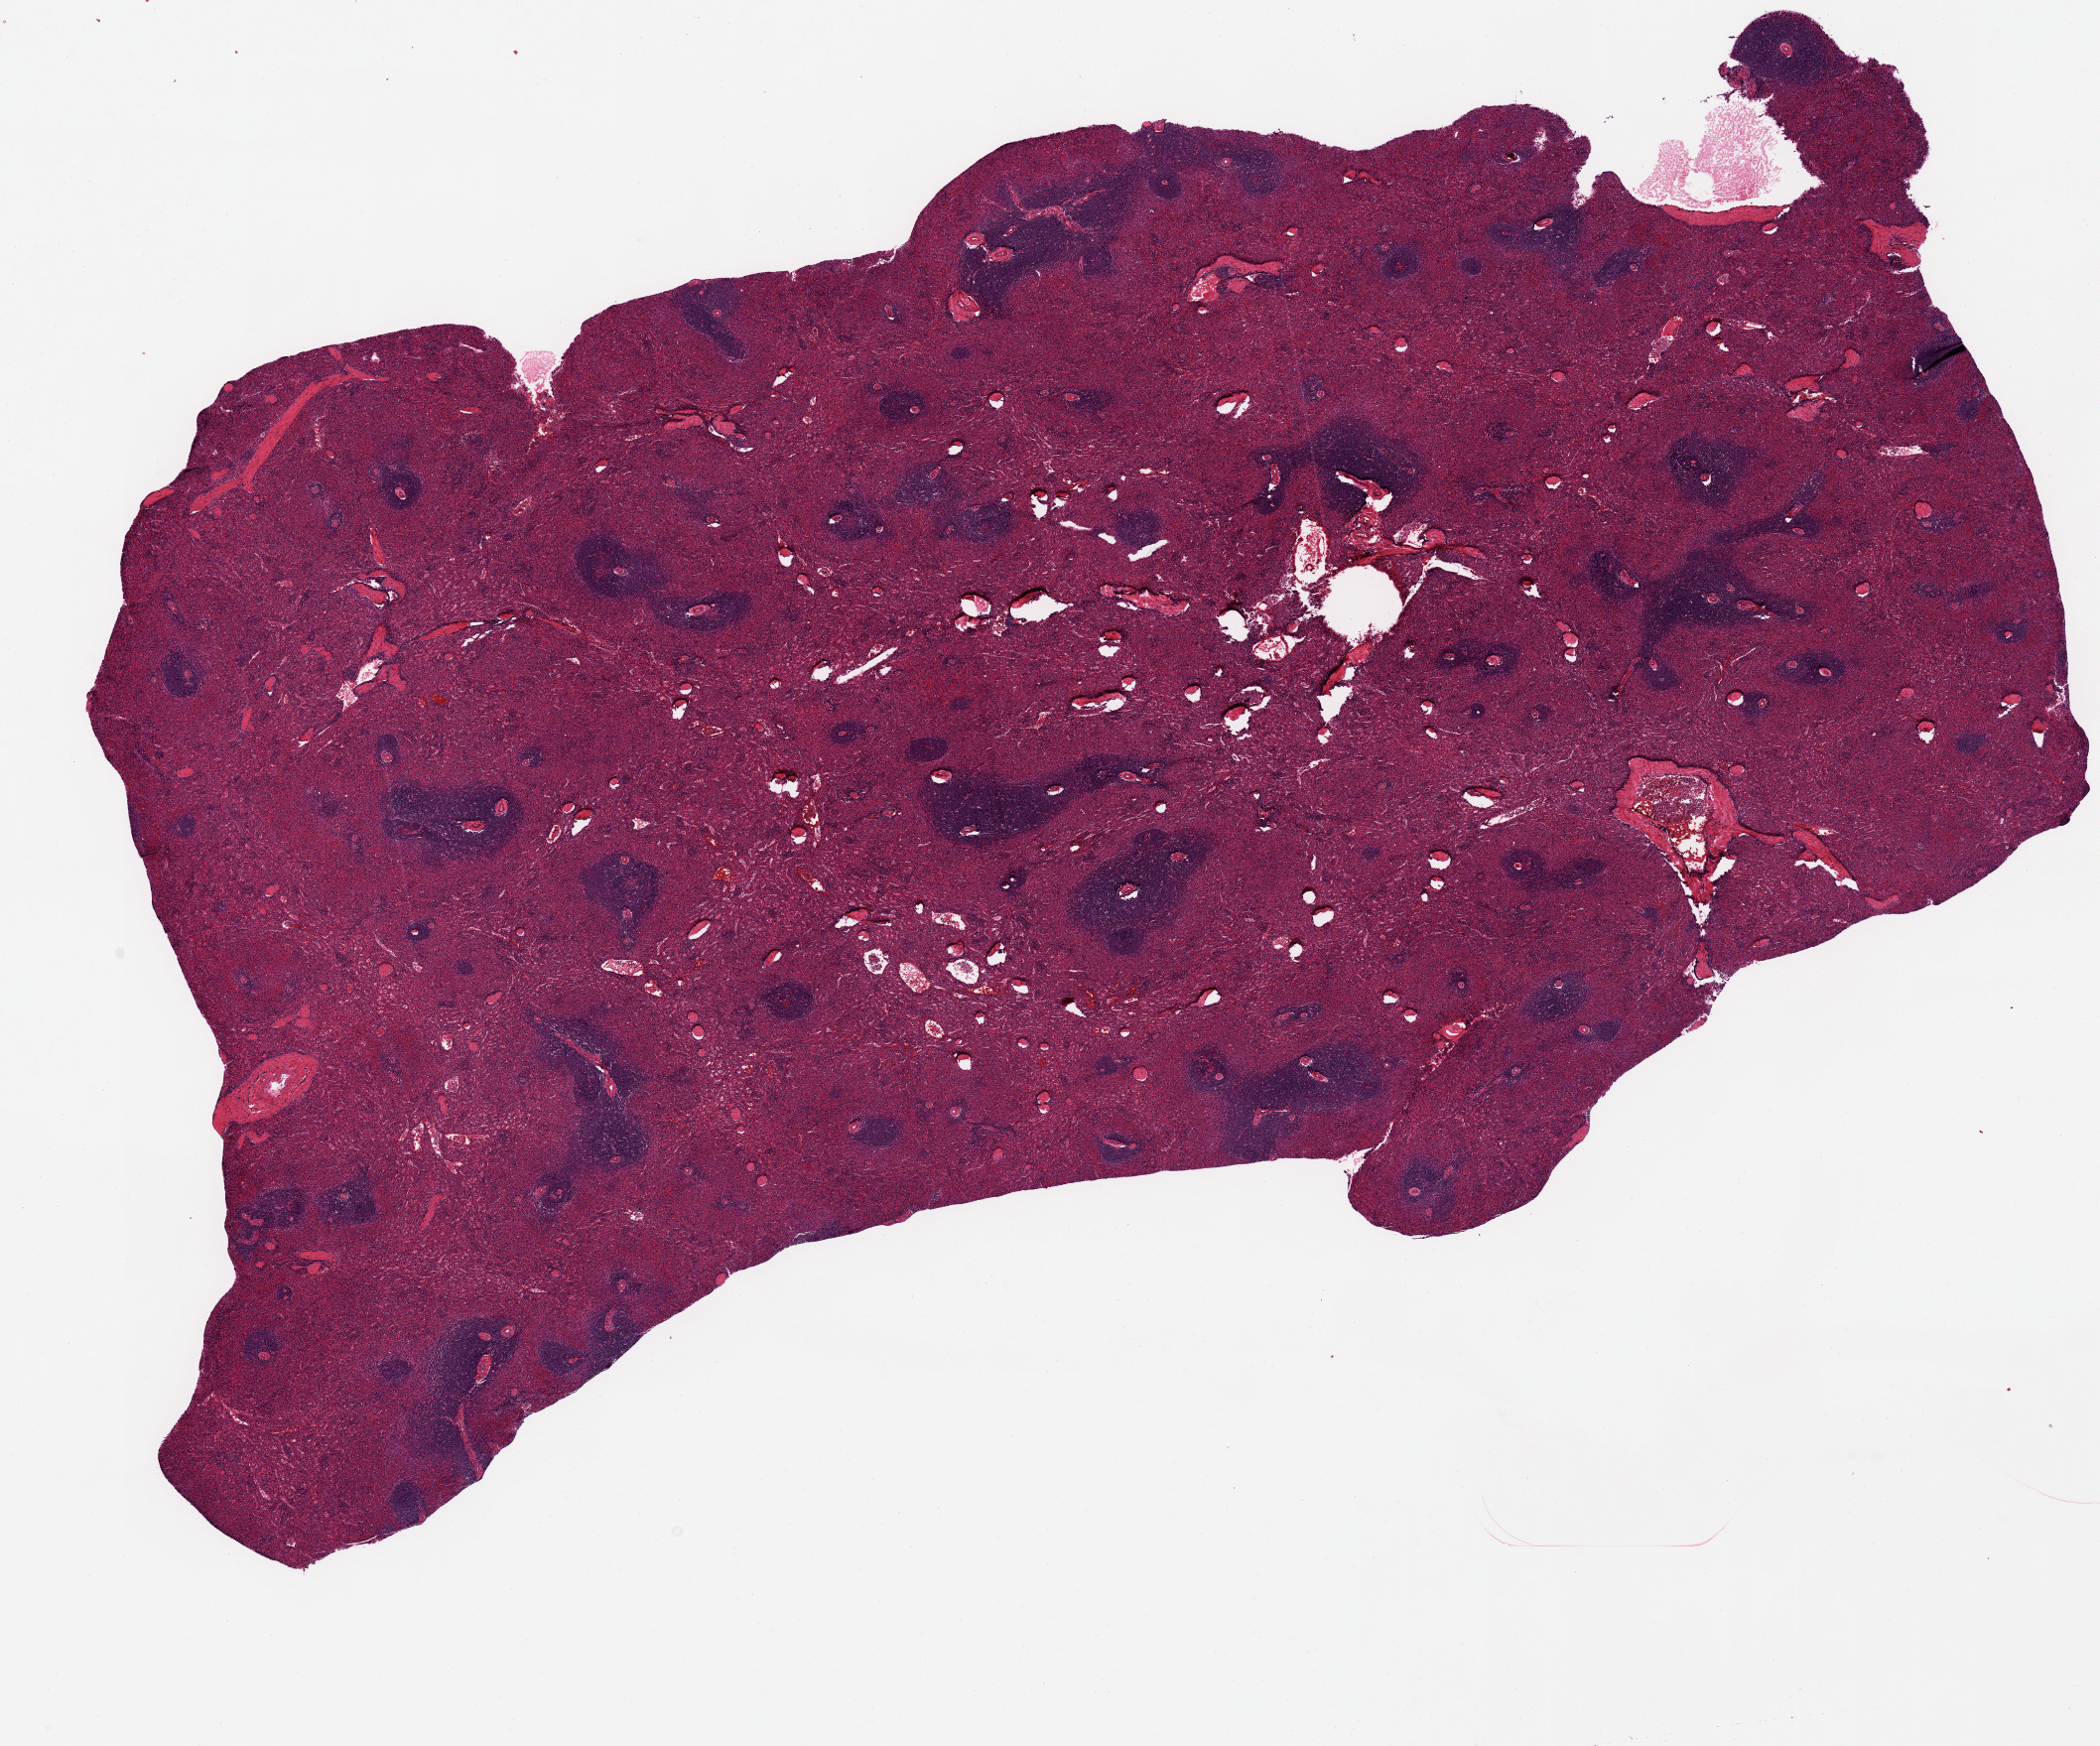
Whole-slide image, hematoxylin and eosin (H&E) stain, brightfield — shown as a low-resolution overview of the whole scanned area (about 16.7 x 13.9 mm), PAXgene-fixed, paraffin-embedded tissue, target tissue: spleen, tissue donor sample. Male donor.
Reviewer comment on this tissue sample: Mild congestion.